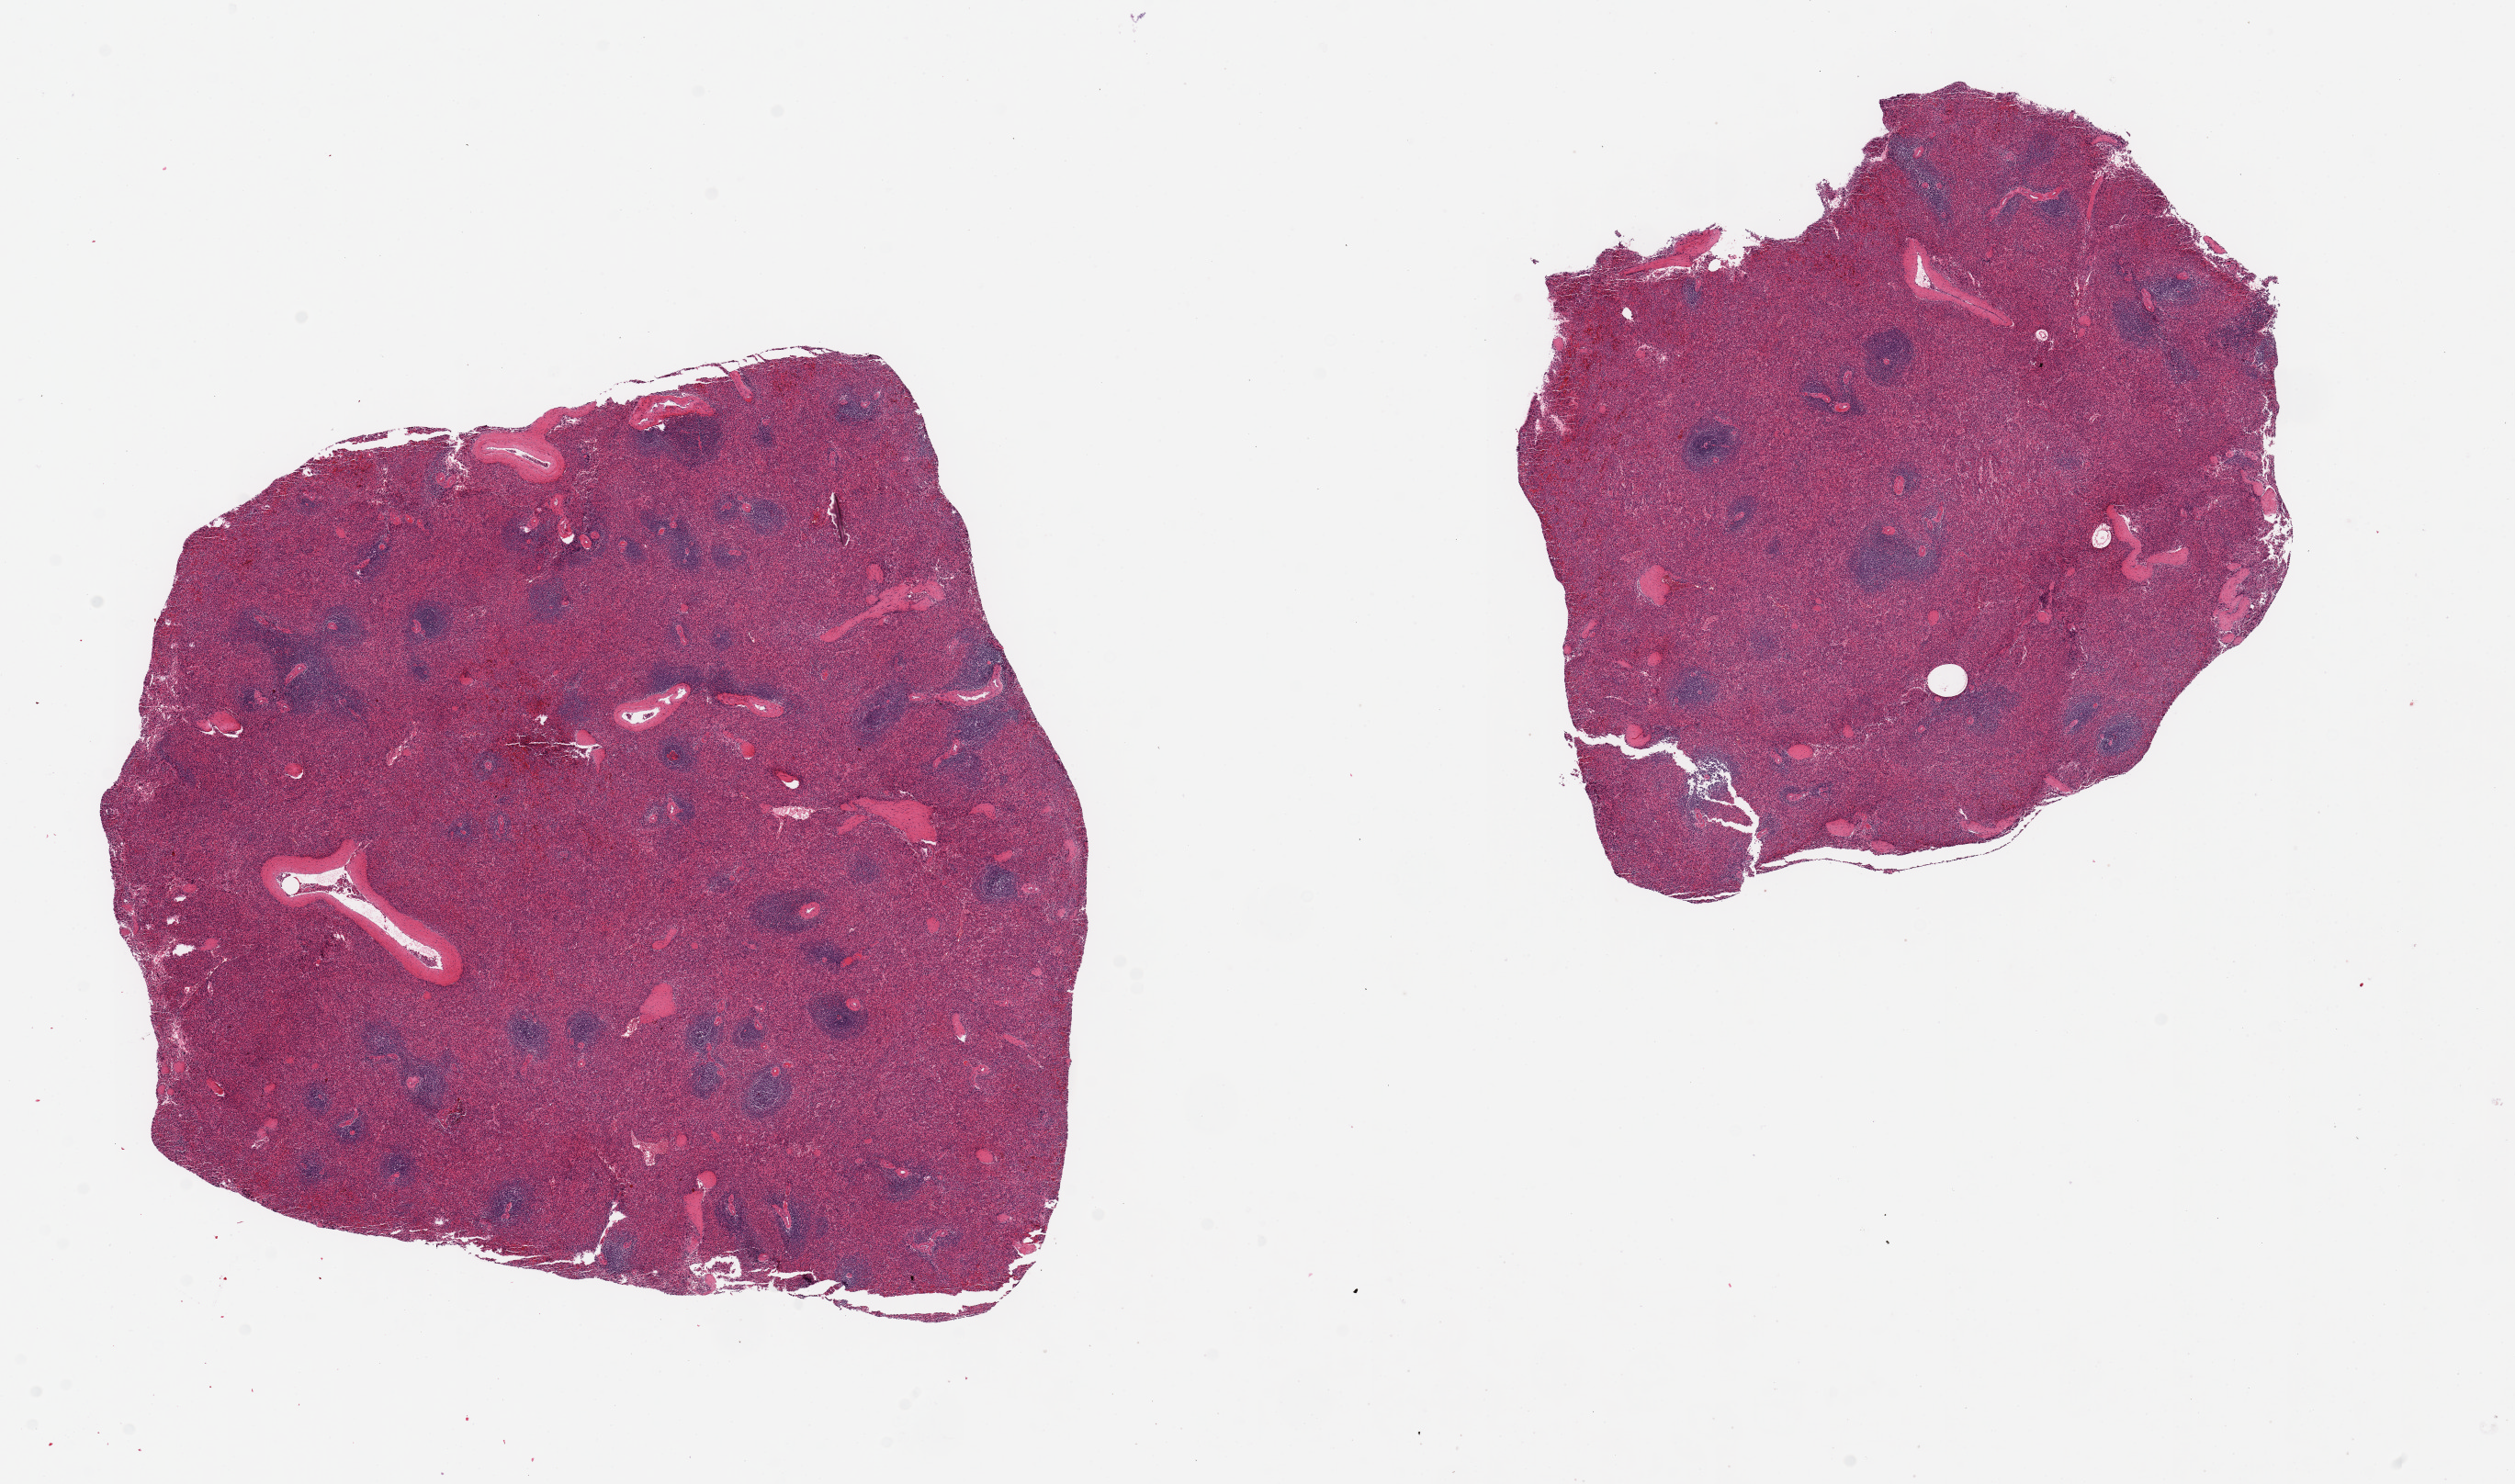
Digitized hematoxylin and eosin (H&E)-stained section, whole scanned area (about 21.7 x 12.8 mm) shown as a low-resolution overview, PAXgene-fixed, paraffin-embedded tissue, target tissue: spleen, donor tissue sample. Male donor.
* reviewer comment on this tissue sample: 2 pieces, 9x8 & 7x6.5mm; mild congestion